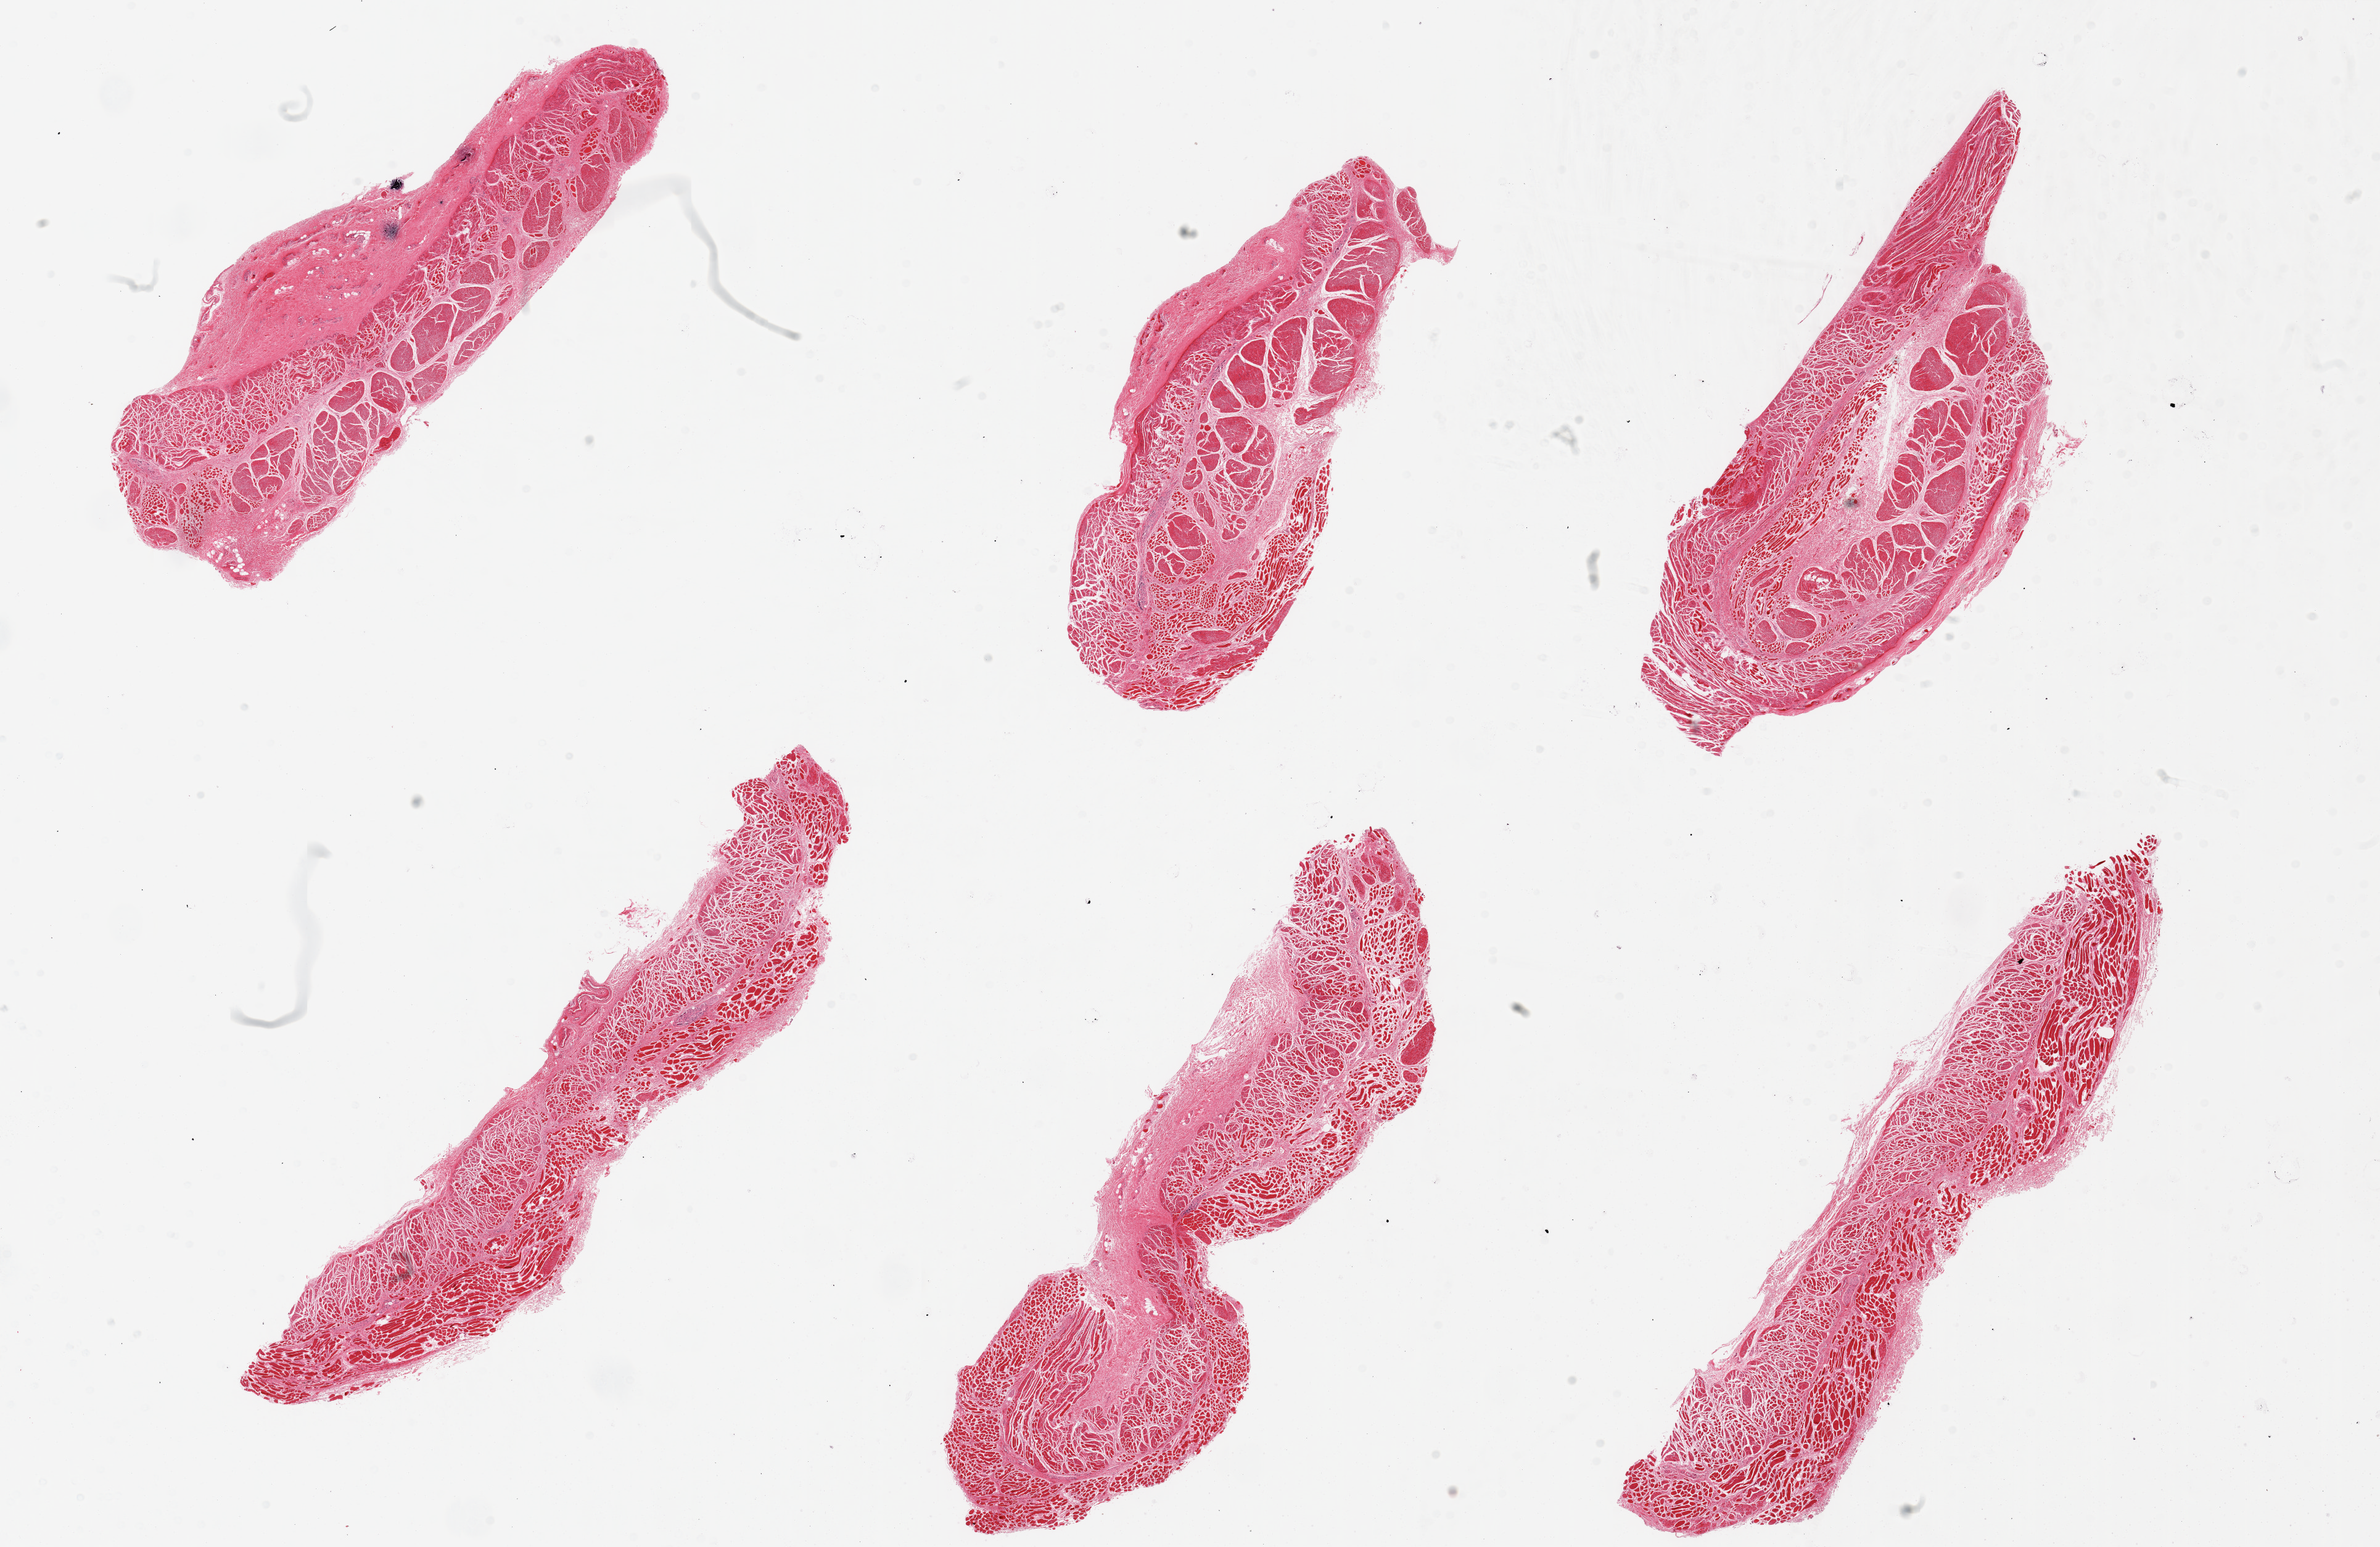
Digitized hematoxylin and eosin (H&E)-stained section, shown as a low-resolution overview of the whole scanned area (about 30.5 x 19.8 mm, slide scanned at 20x), PAXgene-fixed, paraffin-embedded tissue, sampled site (target tissue): esophageal muscle, tissue donor sample. Male donor.
Pathologist's review note for this sample: 6 pieces, all muscularis.